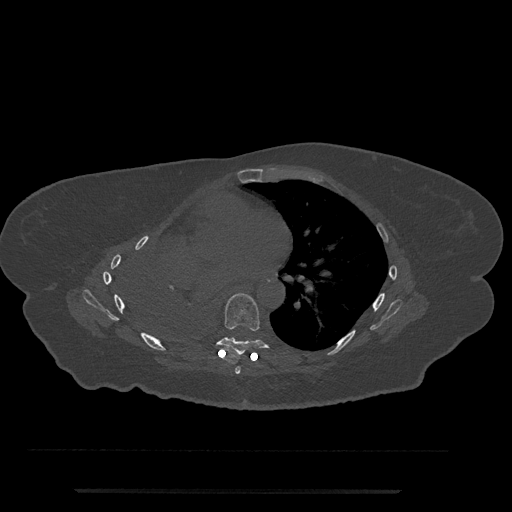
CT including the spine, one axial slice. Slice 442 of 797 in the series (ordered by position). 120 kVp. Bone window (W 1800 / L 400 HU). 0.5 mm slice thickness. 512 × 512 image matrix, field of view 440 × 440 mm. Patient: female, 51 years. Case-level facts recorded for this patient, not image findings: primary cancer: neuro; vertebrae with lytic lesions (as recorded): T8.
Structures marked on this image (semi-automatic segmentation, software-assisted and operator-edited):
- T6 vertebra: box from (x=235, y=366) to (x=241, y=374) px
- T7 vertebra: (x=207, y=293)–(x=278, y=355)